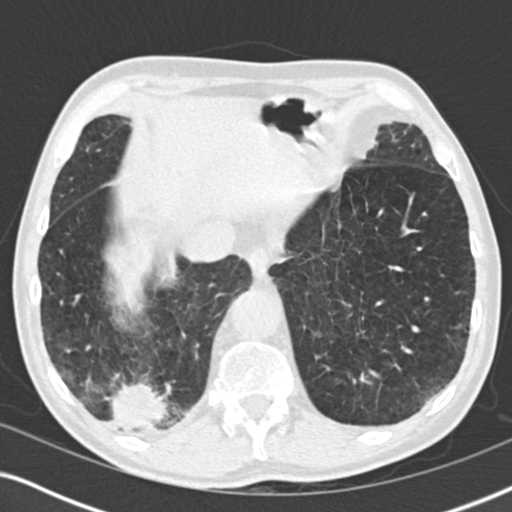
Low-dose screening chest CT, one axial slice; position 53 of 196 along the scan axis; reconstruction kernel B30f; lung window (W 1500 / L -600 HU); 2 mm slice thickness; 512 × 512 image matrix.
Structures marked on this image (manually delineated by an expert):
- lesion 3 (tumor, lower lobe of right lung): bounding box (x1, y1, x2, y2) in pixels: (107, 382, 167, 430)